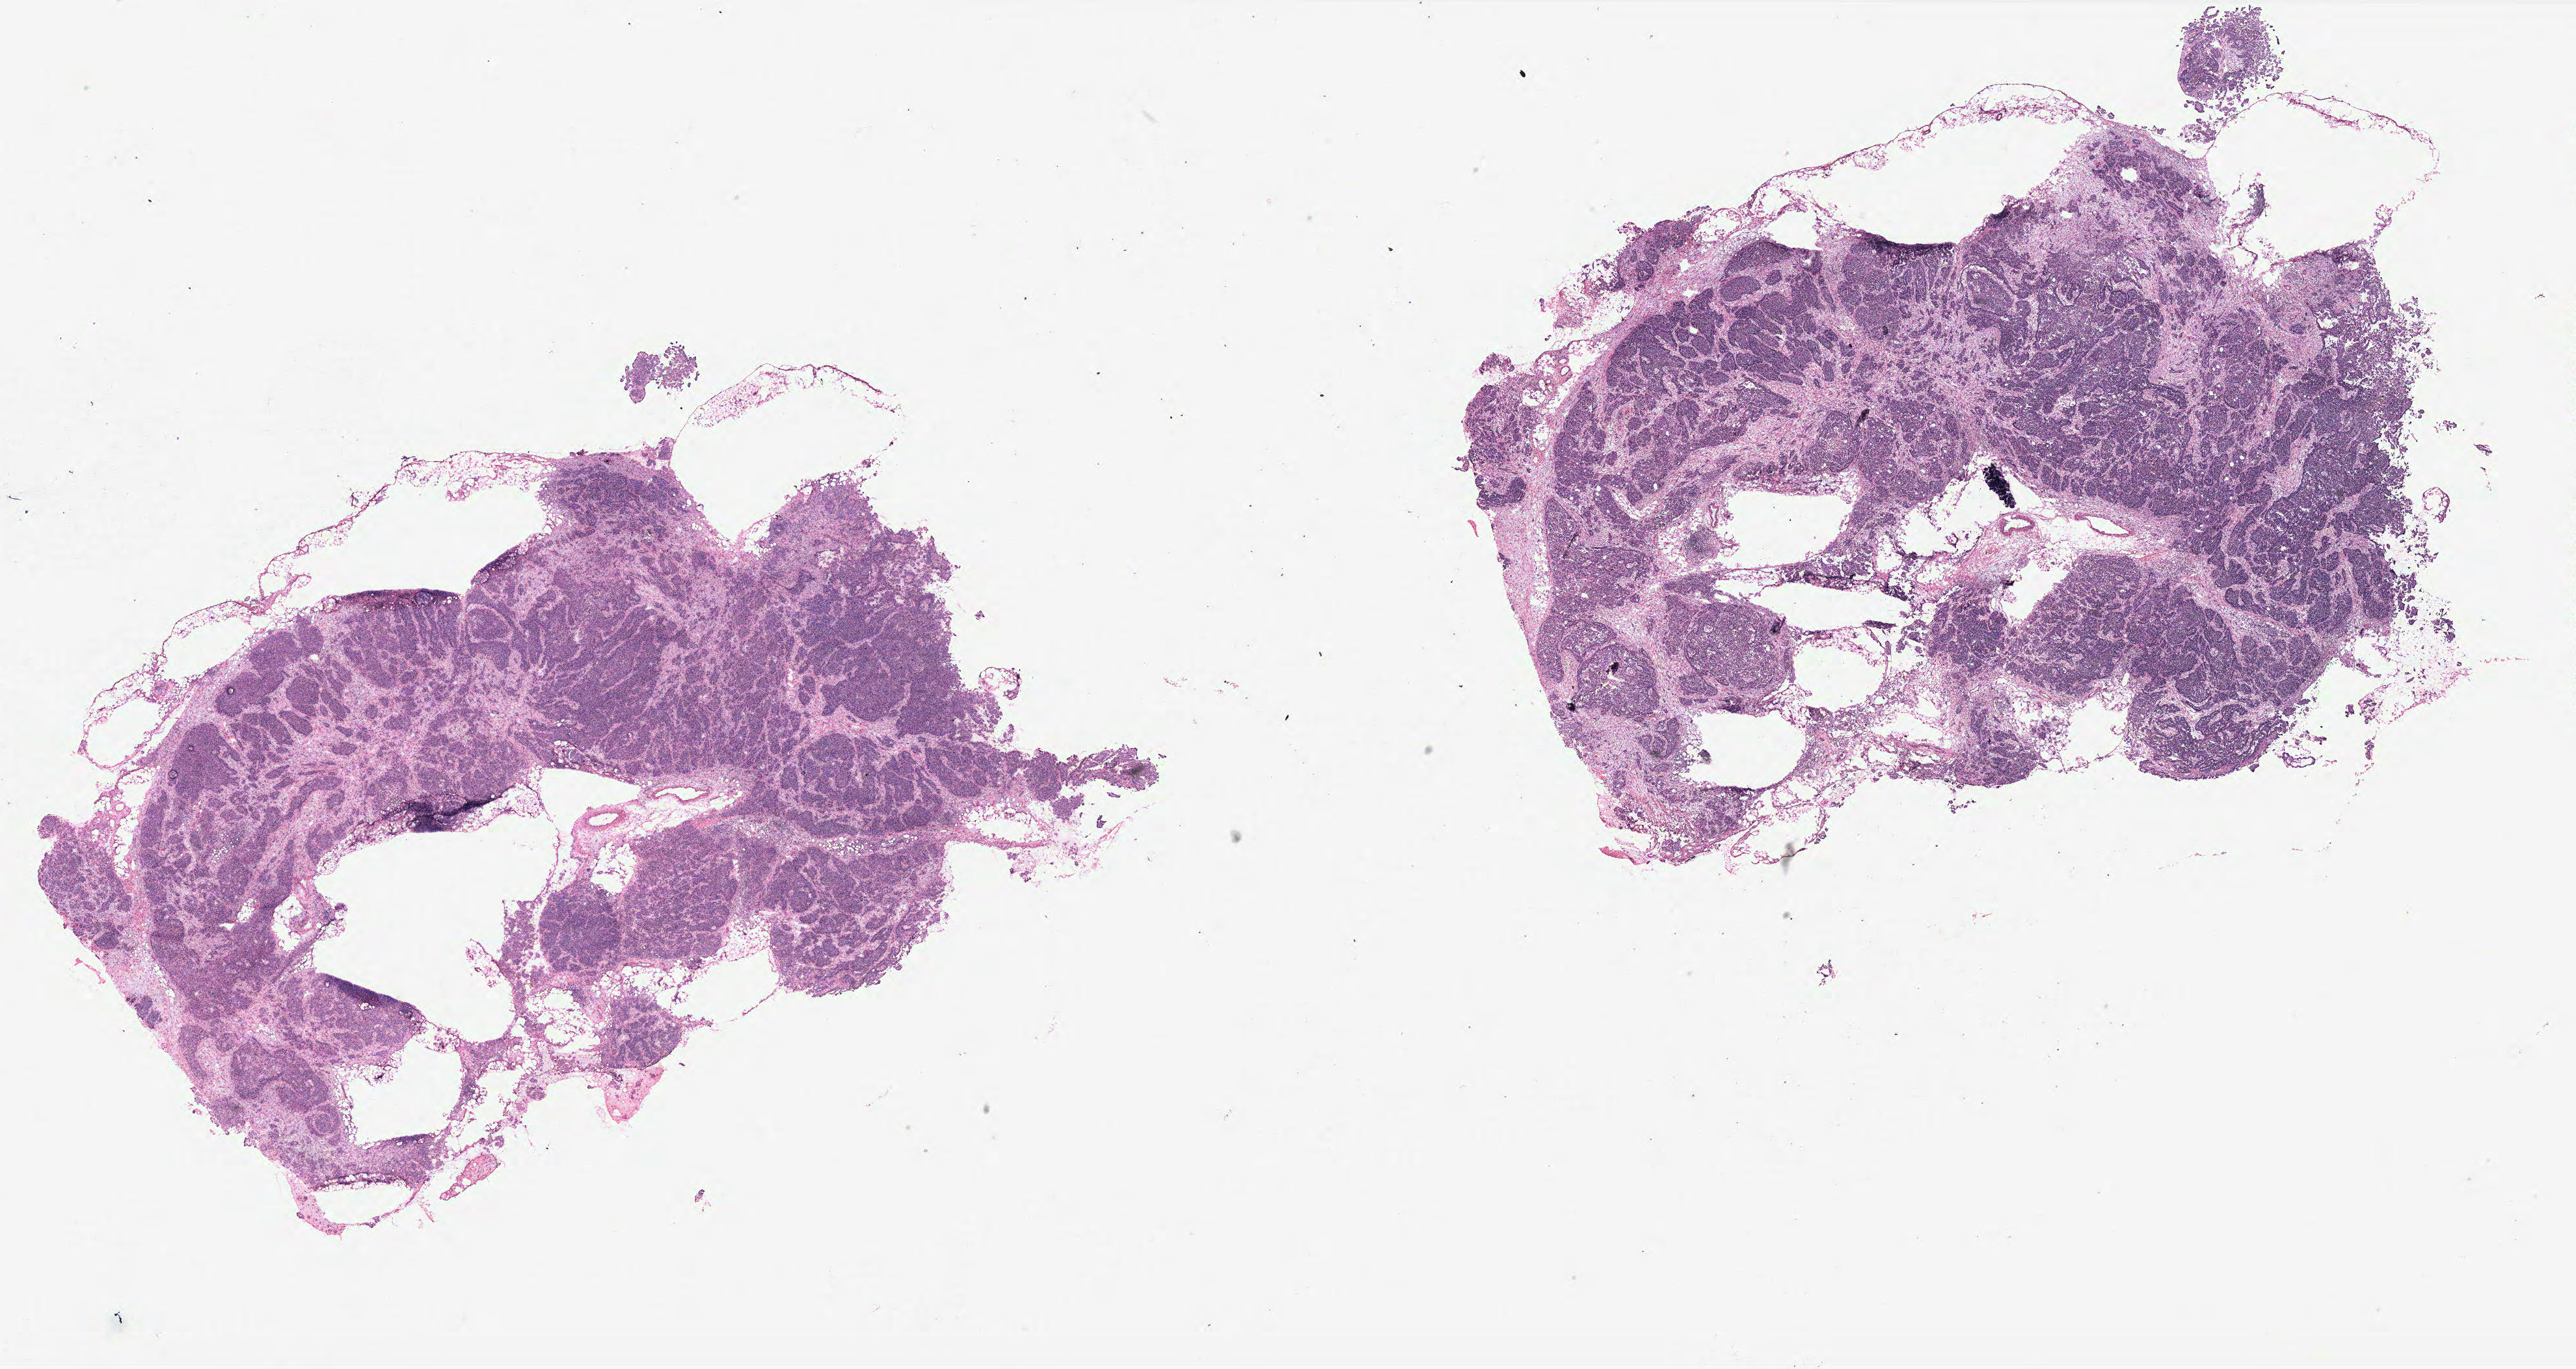
Digitized Hematoxylin and eosin (H&E) stained tissue section (whole slide) — whole scanned area (about 31.7 x 16.8 mm) shown as a low-resolution overview. Ovary, tissue type not recorded.
Patient diagnosis (cohort enrolment): ovarian cancer (ovary).